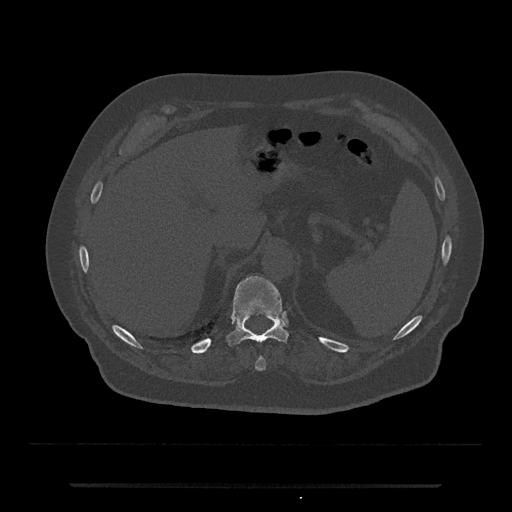
CT including the spine, one axial slice; slice 655 of 797 in the series (ordered by position); 120 kVp; bone window (W 1800 / L 400 HU); 512 × 512 image matrix, field of view 434 × 434 mm. Male patient, age 80 years. Case-level facts recorded for this patient, not image findings: primary cancer: prostate.
Outlined on this slice (semi-automatic segmentation, software-assisted and operator-edited):
- T10 vertebra: bounding box <255,357,266,371> (left, top, right, bottom; pixels)
- T11 vertebra: <226,275,288,345>